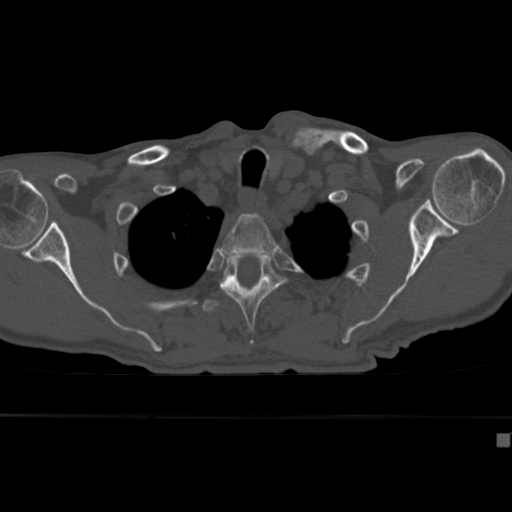
CT including the spine, one axial slice; slice 334 of 430 in the series (ordered by position); reconstruction kernel Br40s; bone window (W 1800 / L 400 HU); 1.5 mm slice thickness; 512 × 512 image matrix, field of view 337 × 337 mm. Patient: male, 64 years. From the clinical record (not read from this slice): primary cancer: uterus.
Structures marked on this image (semi-automatic segmentation, software-assisted and operator-edited):
- T2 vertebra: bounding box (x1, y1, x2, y2) in pixels: (220, 213, 278, 258)
- T3 vertebra: (220, 252, 287, 344)
- T4 vertebra: (202, 299, 220, 313)